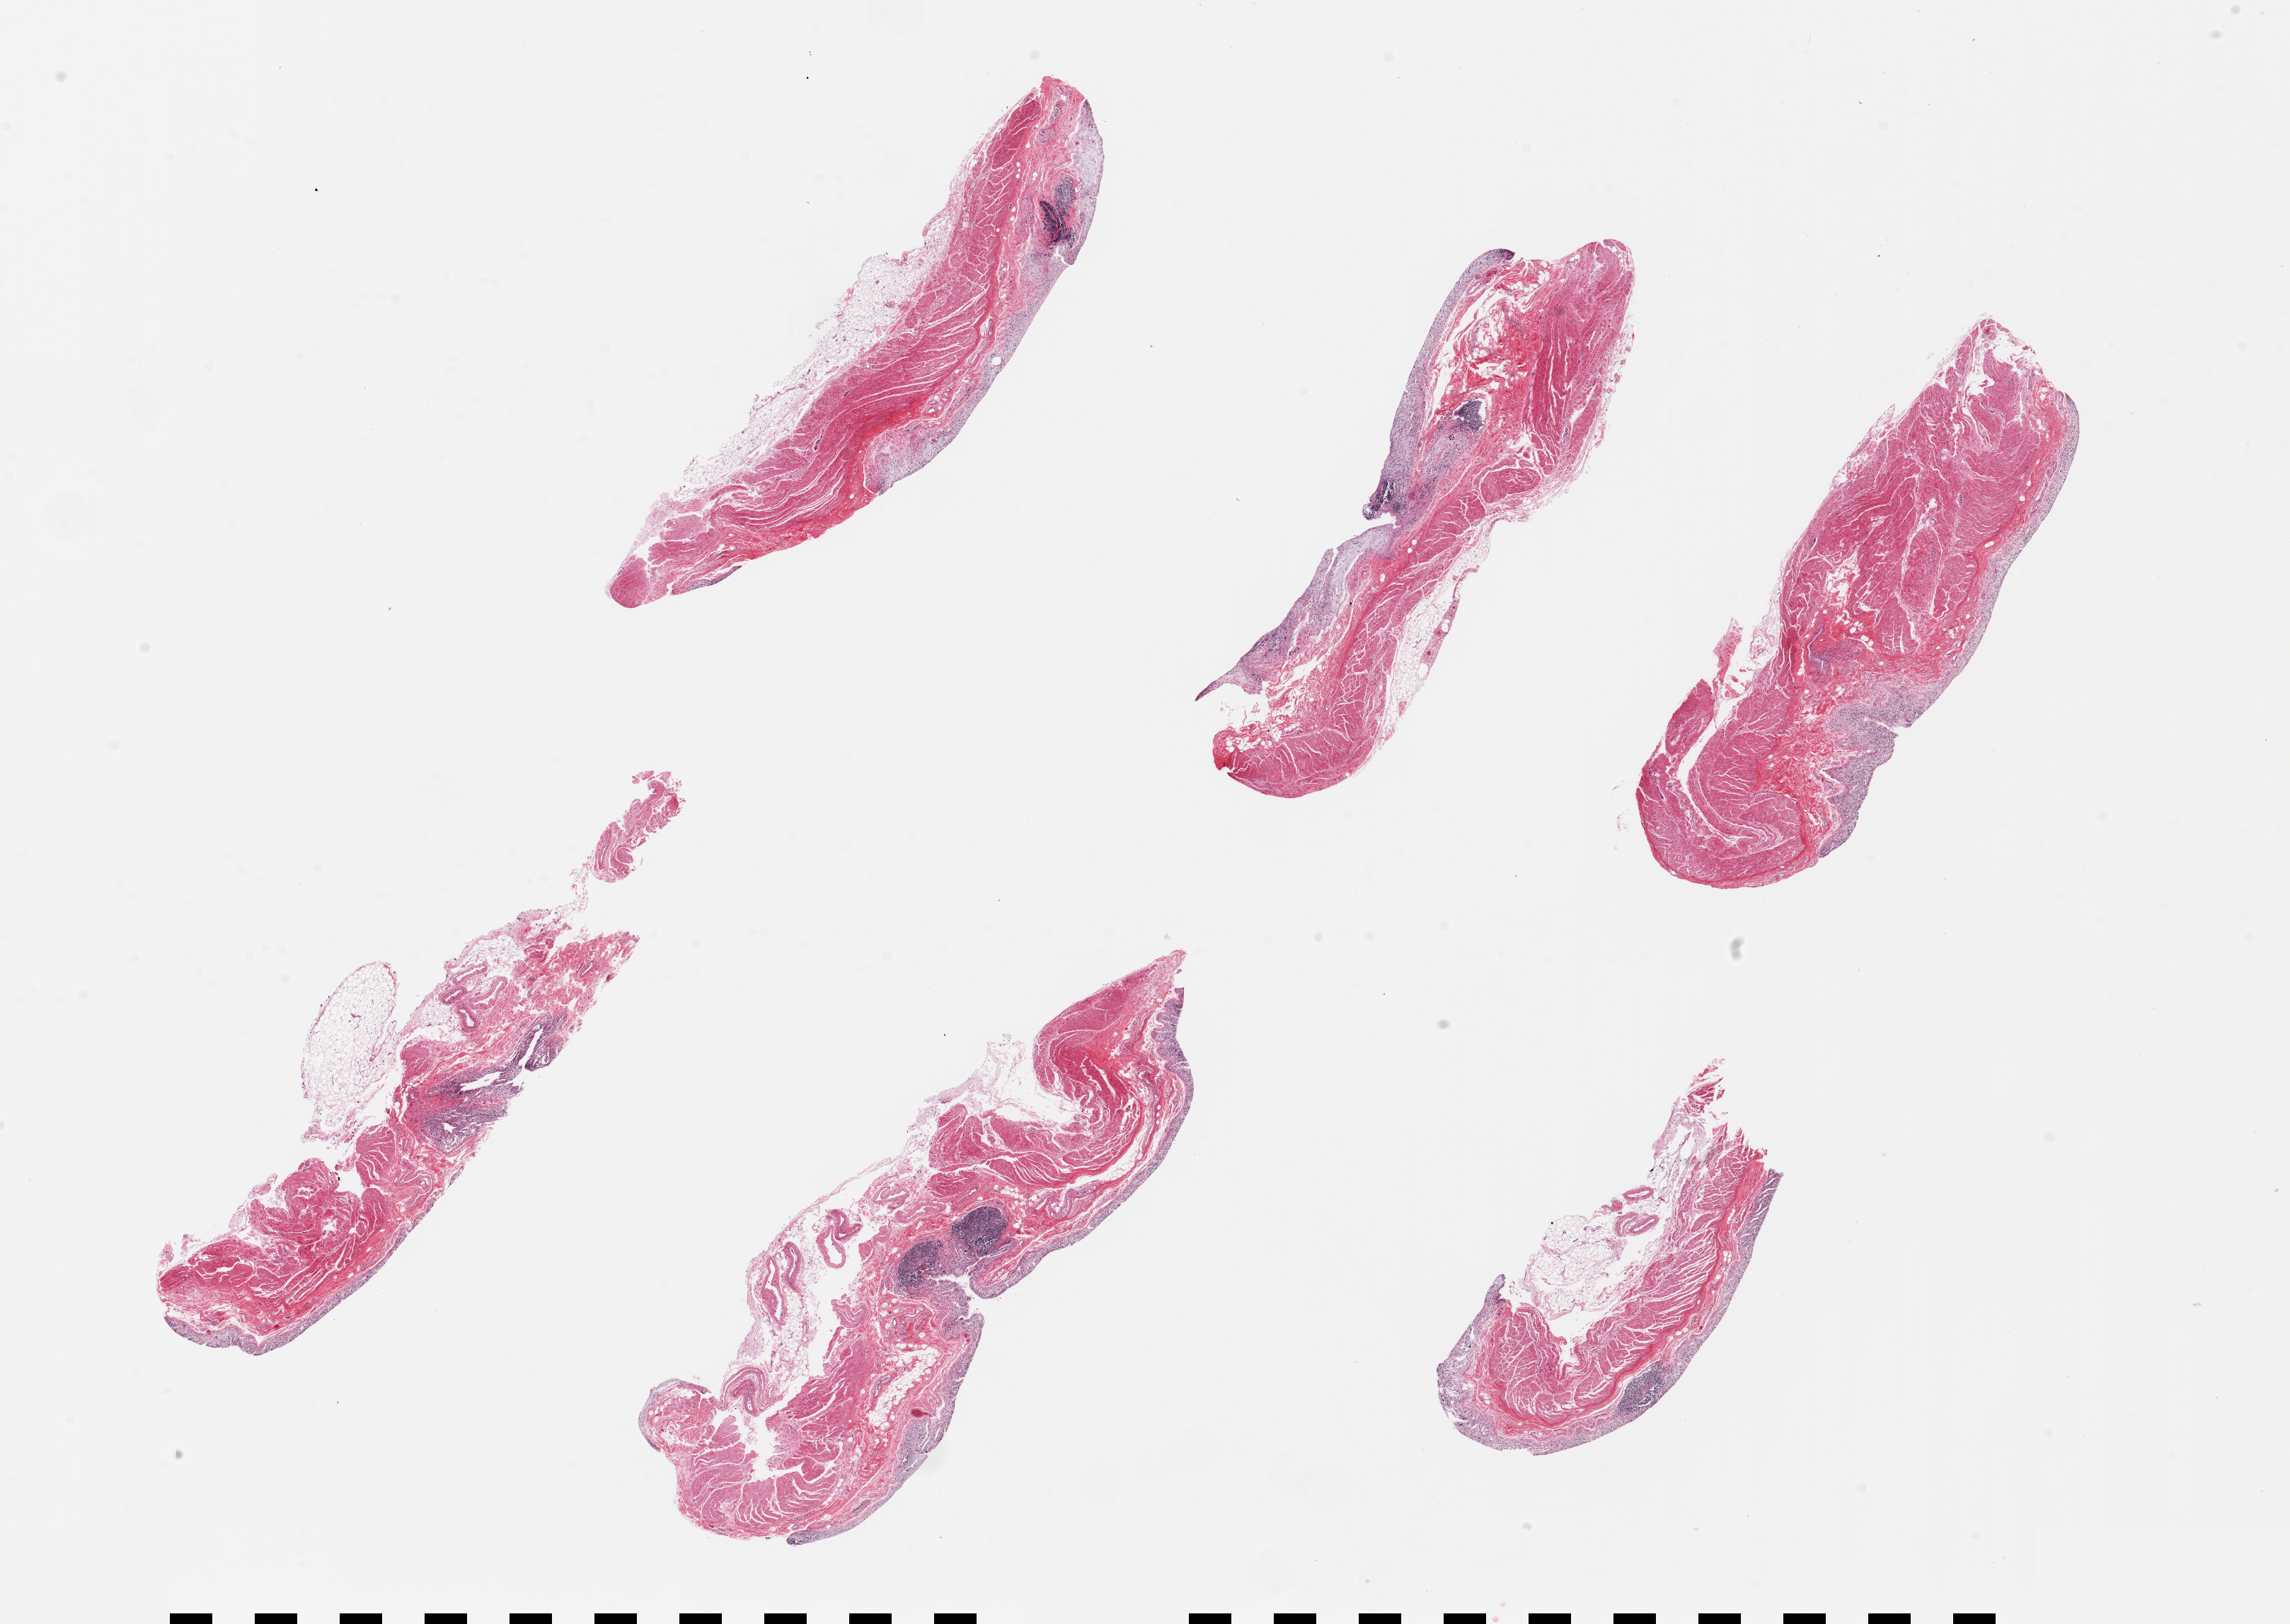
Whole-slide image, haematoxylin and eosin stain, brightfield, low-resolution overview of the scanned area, about 25.6 x 18.2 mm (from a 20x scan), PAXgene-fixed, paraffin-embedded tissue, sampled site (target tissue): transverse colon, tissue donor sample. Donor: female.
Review note (as recorded): 6 pieces ~7x2mm, mucosa near totally sloughed, badly autolyzed.